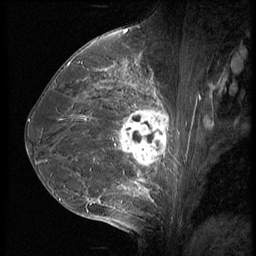
Breast MRI (dynamic contrast-enhanced), one sagittal slice. Slice 32 of 56 in the series (ordered by position). 3 images stored at this slice position (order not interpretable as contrast timing). 1.5 T. TE 4.2 ms, TR 9 ms. 2.5 mm slice thickness. 256 × 256 image matrix, field of view 180 × 180 mm. Patient: female, 35 years. From the clinical record (not read from this slice): setting: breast cancer imaged before/during neoadjuvant chemotherapy; receptor status: HR-positive, HER2-negative.
Annotated regions visible in this slice (semi-automatically segmented with operator editing):
- analysis volume of interest (the breast-tissue region the enhancement analysis was run in; not a lesion): bounding box <63,60,190,218> (left, top, right, bottom; pixels)
- tumour enhancement mask (voxels above the 140 % enhancement threshold inside the analysis volume of interest): <86,76,169,203>